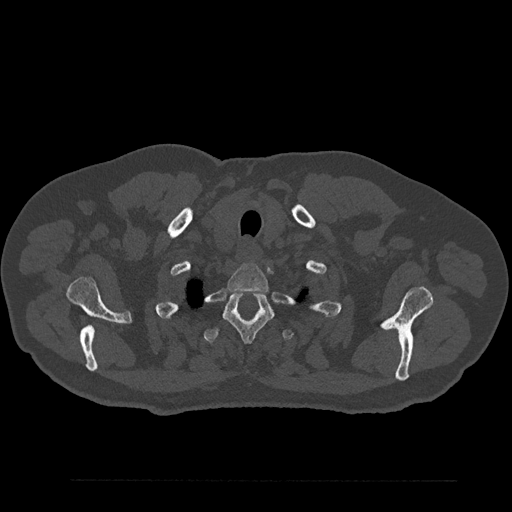
CT including the spine, one axial slice; reconstruction kernel Br40s/3; 120 kVp; bone window (W 1800 / L 400 HU); 0.5 mm slice thickness; 512 × 512 image matrix, field of view 430 × 430 mm. Patient: male, 61 years. Case-level facts recorded for this patient, not image findings: primary cancer: prostate.
Outlined on this slice (semi-automatically segmented with operator editing):
- T1 vertebra: bounding box [x1, y1, x2, y2] px = [227, 263, 269, 293]
- T2 vertebra: [223, 292, 273, 343]
- T3 vertebra: [204, 327, 294, 344]